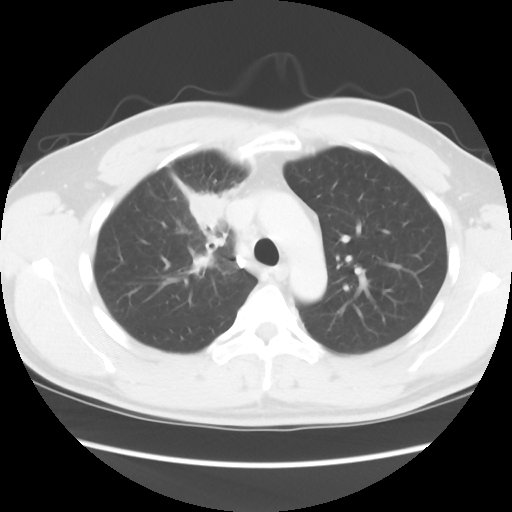
Chest CT, one axial slice. Slice 64 of 80 in the series (ordered by position). Reconstruction kernel STANDARD. 120 kVp. Lung window (W 1500 / L -600 HU). 512 × 512 image matrix, field of view 360 × 360 mm. Patient: male, 35 years. Case-level facts recorded for this patient, not image findings: clinical TNM (as recorded): T1c N1 M1b.
Structures marked on this image (bounding box drawn by a radiologist):
- lung tumour (recorded histology: adenocarcinoma): bounding box [x1, y1, x2, y2] px = [184, 186, 230, 237]